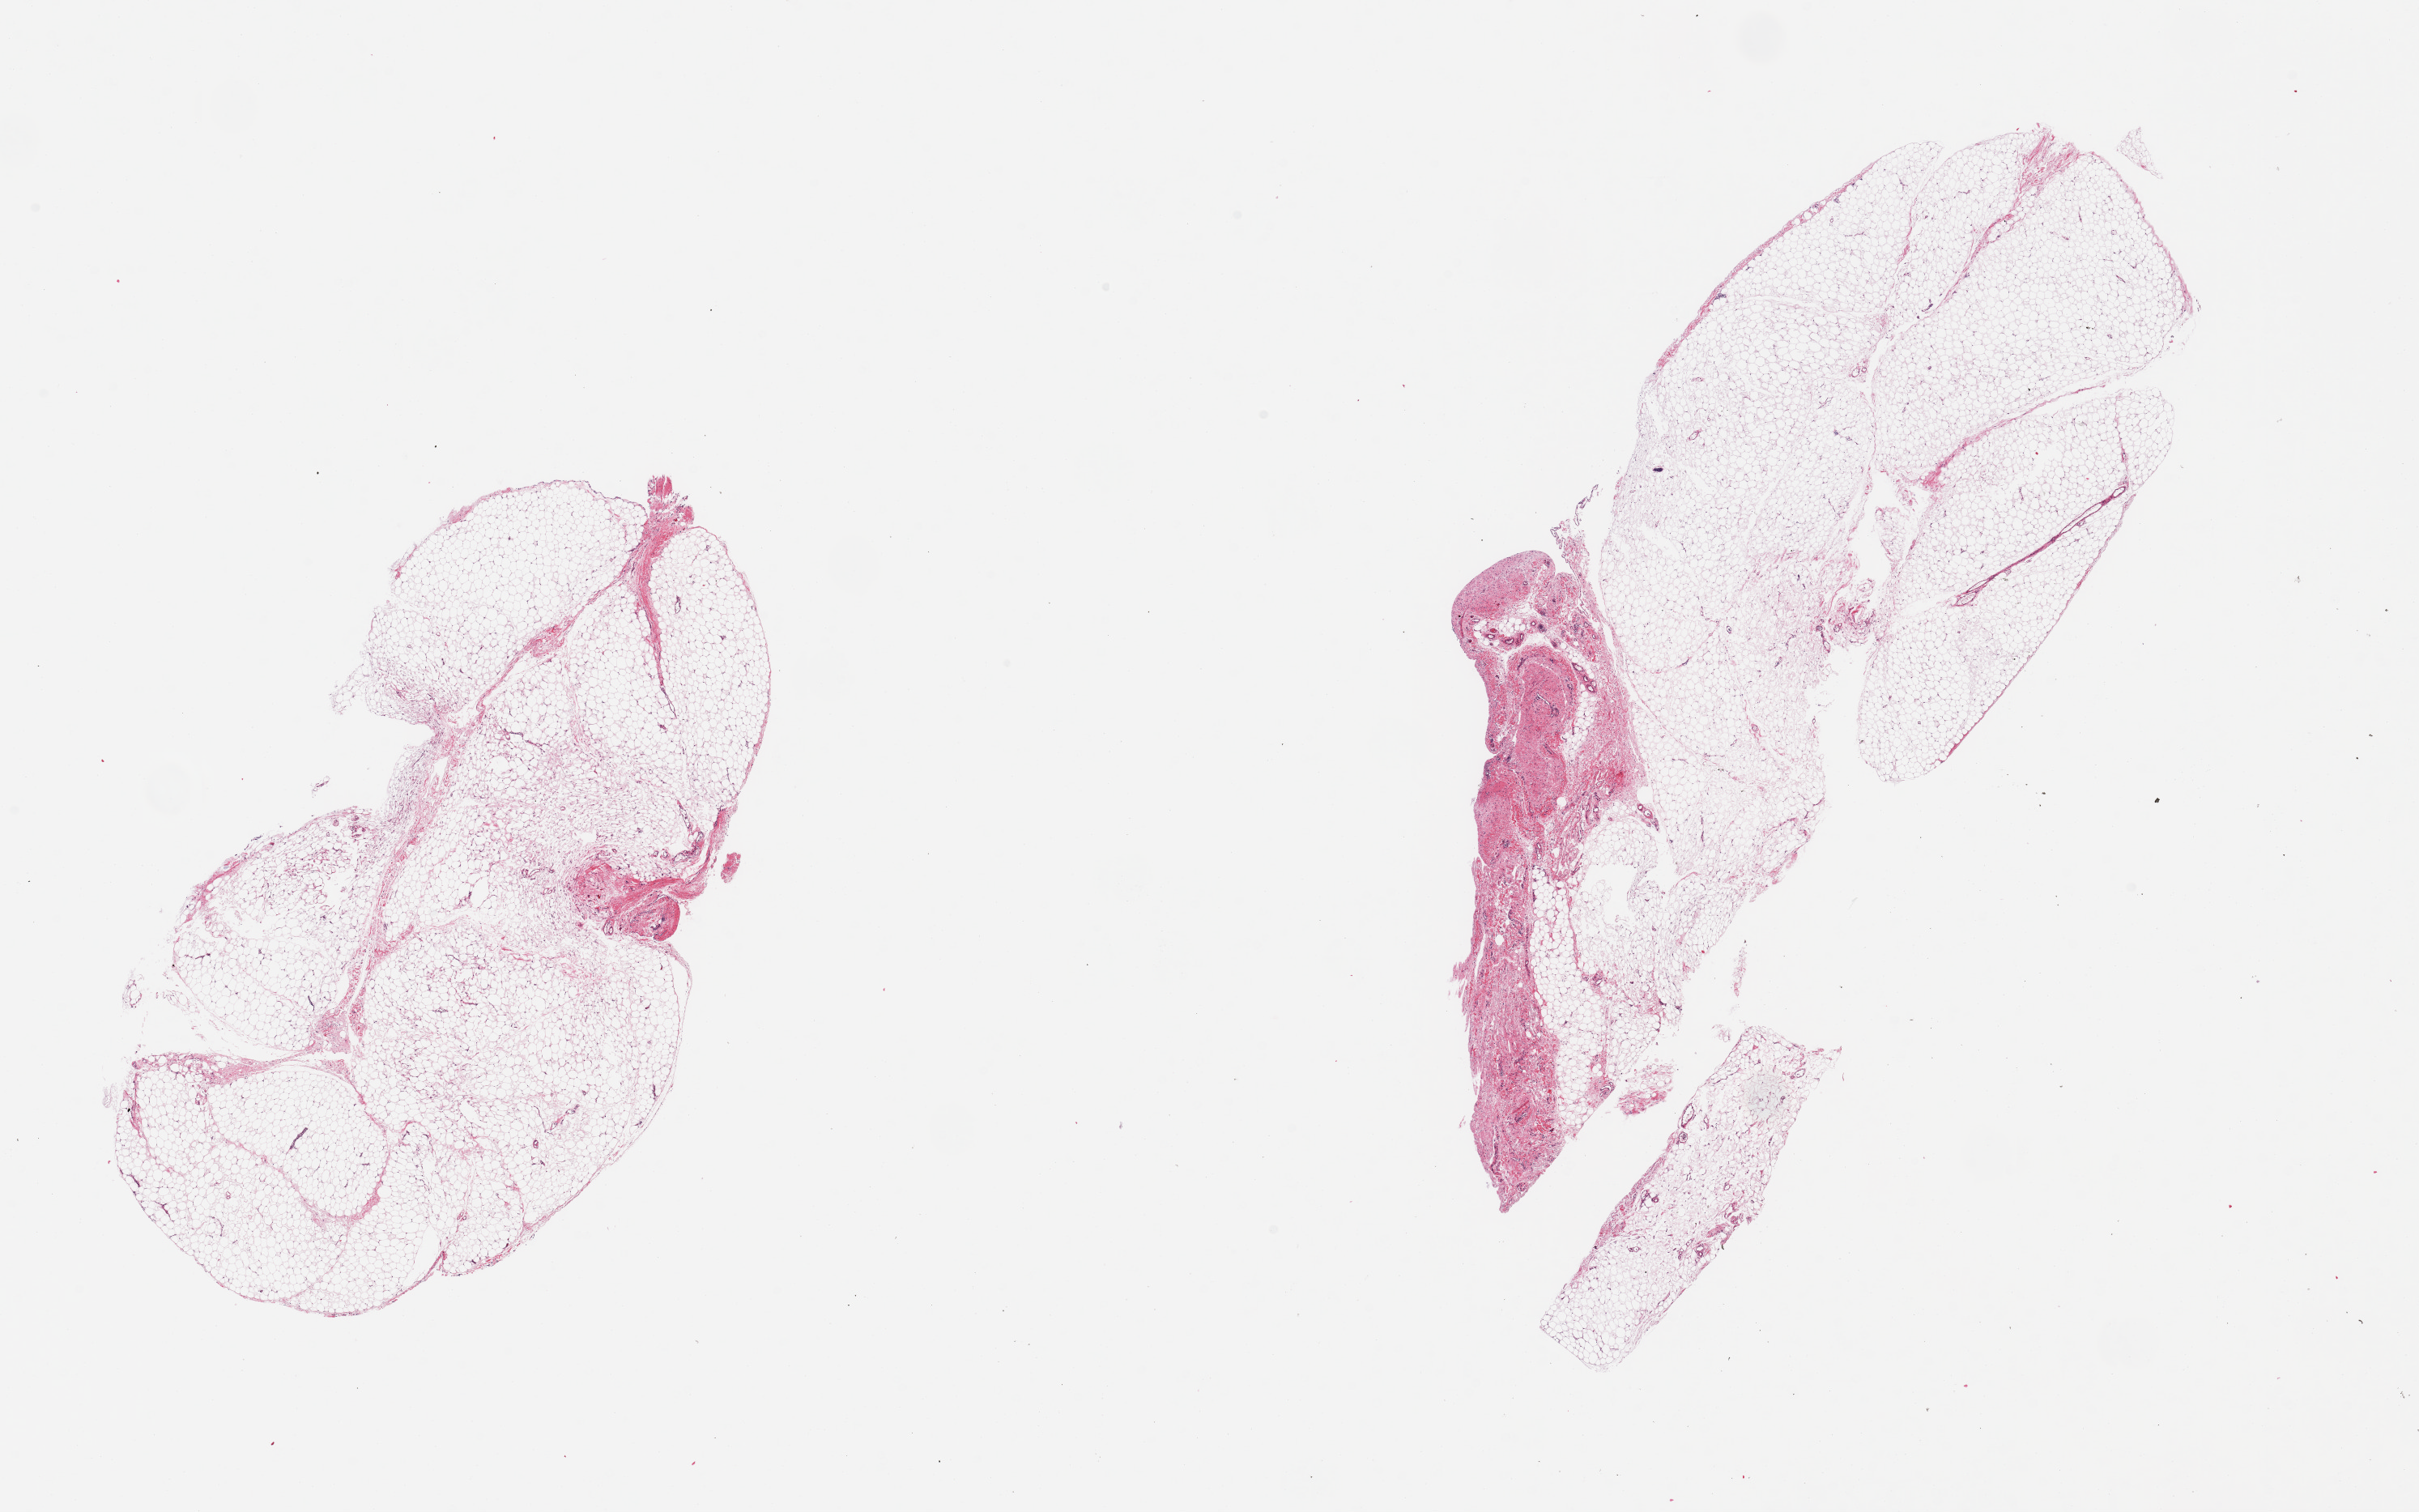
Digitized hematoxylin and eosin (H&E)-stained section — shown as a low-resolution overview of the whole scanned area (about 23.6 x 14.8 mm); PAXgene-fixed paraffin-embedded (PFPE) section; section of omentum (target tissue); tissue donor sample. Male donor.
- reviewer comment on this tissue sample: 2 pieces; 10% & 5% fibrous content